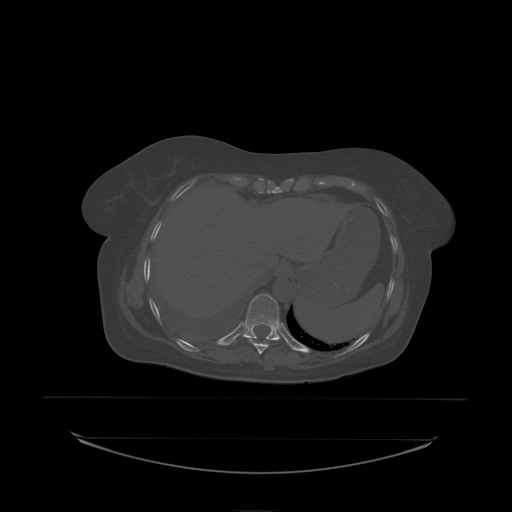
CT including the spine, one axial slice; position 118 of 242 along the scan axis; bone window (W 1800 / L 400 HU); 512 × 512 image matrix, field of view 500 × 500 mm. Patient: female, 53 years. From the clinical record (not read from this slice): primary cancer: lung; vertebrae with lytic lesions (as recorded): T7, L1.
Outlined on this slice (semi-automatic segmentation, software-assisted and operator-edited):
- T10 vertebra: bounding box [x1, y1, x2, y2] px = [243, 294, 280, 338]